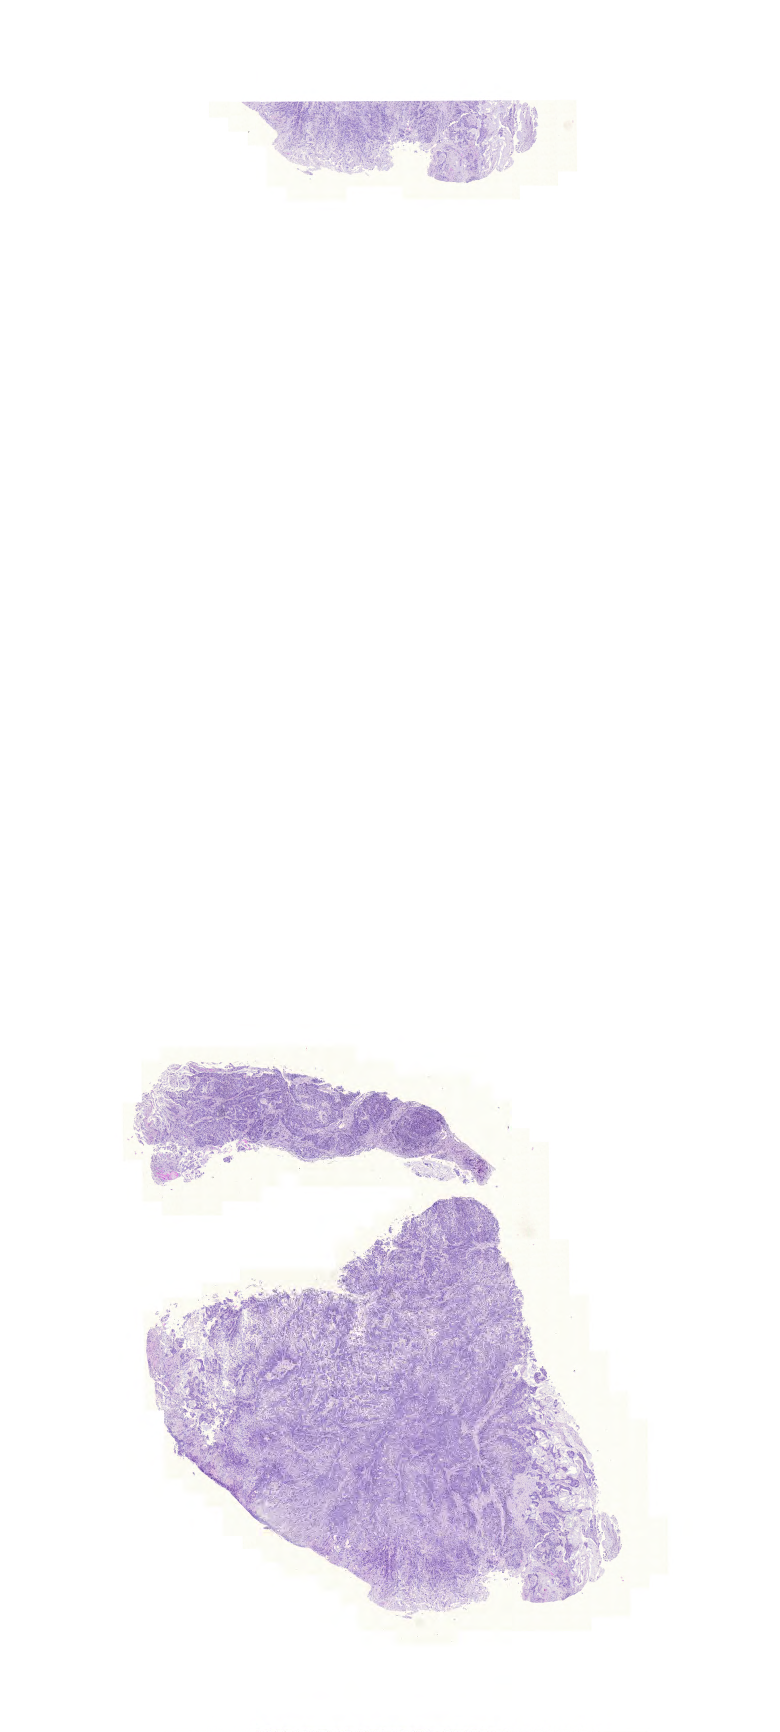
Digitized Hematoxylin and eosin (H&E) stained tissue section (whole slide), shown as a low-resolution overview of the whole scanned area (about 11.6 x 25.8 mm, slide scanned at 20x); formalin-fixed paraffin-embedded (FFPE) diagnostic section; colon, primary tumour sample. Patient sex: female.
AJCC pathologic stage: IIIB (6th edition). Pathologic diagnosis: Mucinous adenocarcinoma (ascending colon). Lymph nodes positive (case pathology): 3 of 19 examined.